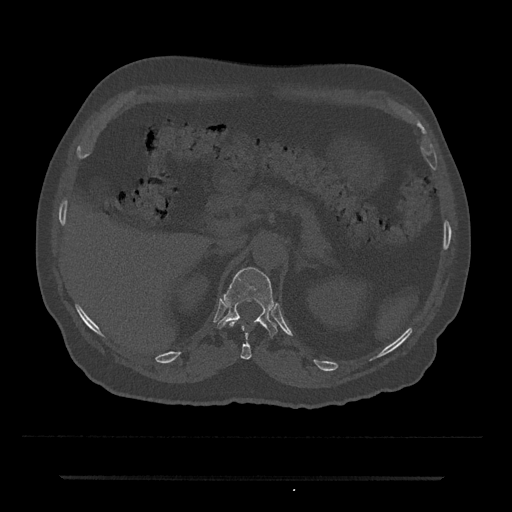
CT including the spine, one axial slice. Reconstruction kernel Br40s/3. 120 kVp. Bone window (W 1800 / L 400 HU). 0.5 mm slice thickness. 512 × 512 image matrix. Male patient, age 69 years. Case-level facts recorded for this patient, not image findings: primary cancer: prostate.
Annotated regions visible in this slice (semi-automatic segmentation, software-assisted and operator-edited):
- T11 vertebra: box from (x=229, y=321) to (x=251, y=360) px
- T12 vertebra: (x=217, y=267)–(x=277, y=338)